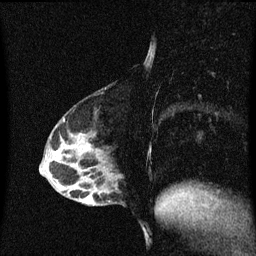
Breast MRI (dynamic contrast-enhanced), one sagittal slice. Position 20 of 60 along the scan axis. Dynamic contrast-enhanced series, image 2 of 3 at this slice position (ordered by acquisition). 1.5 T. TE 4.2 ms, TR 8.4 ms. 2 mm slice thickness. 256 × 256 image matrix, field of view 200 × 200 mm. Female patient, age 40 years.
Annotated regions visible in this slice (semi-automatically segmented with operator editing):
- analysis volume of interest (the breast-tissue region the enhancement analysis was run in; not a lesion): bounding box [x1, y1, x2, y2] px = [82, 172, 121, 207]
- tumour enhancement mask (voxels above the 70 % enhancement threshold inside the analysis volume of interest): [82, 196, 94, 205]